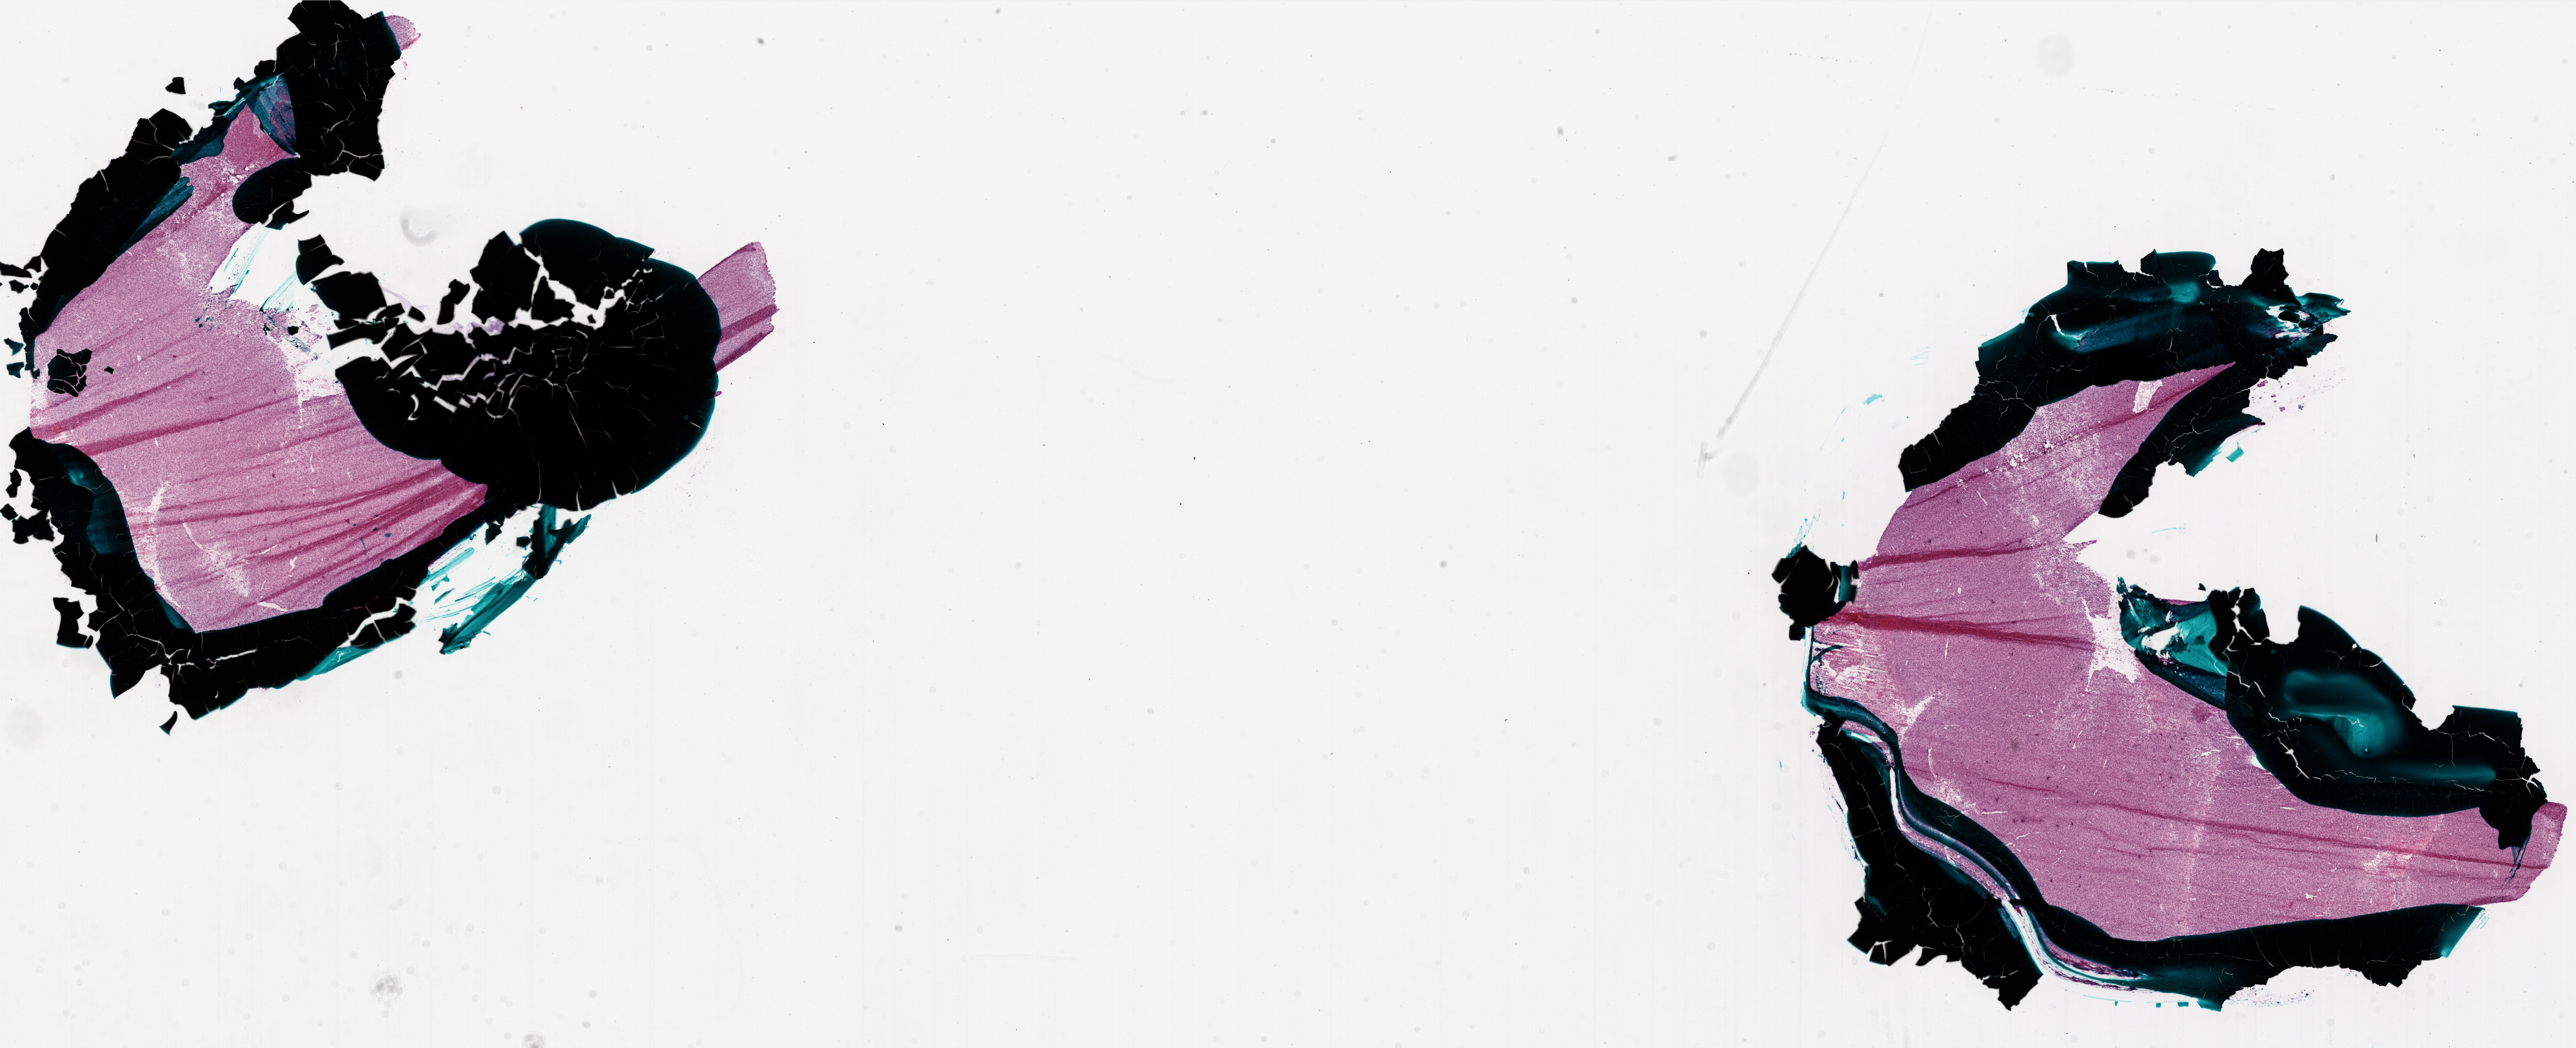
Whole-slide histology image, H&E-stained — shown as a low-resolution overview of the whole scanned area (about 32.0 x 13.0 mm, acquisition: 20x scan), frozen section, sample: primary tumour, brain. Female patient; age at initial diagnosis 53 years. Composition of this section per pathologist review: tumour cells 95%, tumour nuclei 100%, normal cells 0%, stromal cells 0%, necrosis 5%. Inflammatory infiltration, as recorded: lymphocyte infiltration 0%, monocyte infiltration 0%, neutrophil infiltration 0%.
Pathologic diagnosis: Glioblastoma.